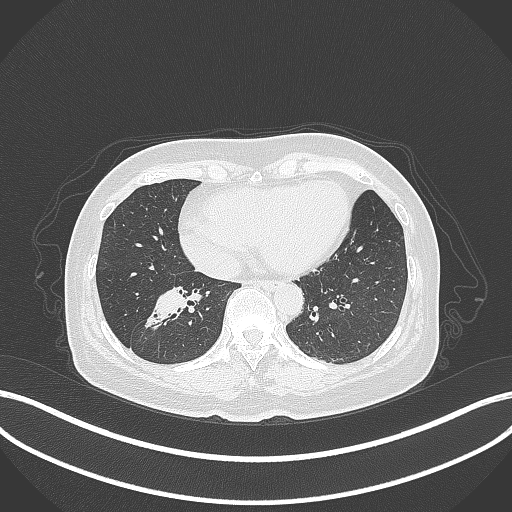
Chest CT, one axial slice. Slice 134 of 429 in the series (ordered by position). 120 kVp. Lung window (W 1500 / L -600 HU). 1 mm slice thickness. 512 × 512 image matrix, field of view 400 × 400 mm. Female patient, age 67 years. From the clinical record (not read from this slice): clinical TNM (as recorded): T1c N1 M0; histopathological grade: G2-3.
Structures marked on this image (rectangle marked by the reading radiologist):
- lung tumour (recorded histology: adenocarcinoma): bounding box [x1, y1, x2, y2] px = [143, 283, 192, 334]